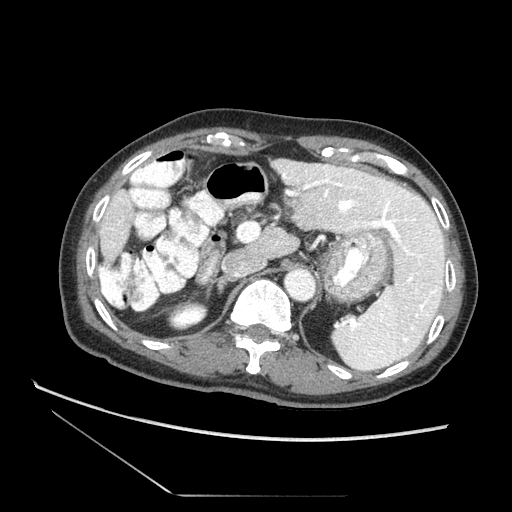
Contrast-enhanced abdominal CT (liver protocol), one axial slice; slice 49 of 73 in the series (ordered by position); soft-tissue window (W 400 / L 40 HU); 2.5 mm slice thickness; 512 × 512 image matrix. Case-level facts recorded for this patient, not image findings: diagnosis: hepatocellular carcinoma (patient treated with transarterial chemoembolisation; whether this scan precedes or follows treatment is not stated here); TNM stage (as recorded): Stage-II.
Annotated regions visible in this slice (semi-automatic segmentation, software-assisted and operator-edited):
- liver parenchyma outside the tumour (the mass and vessels are separate outlines, so this box may not span the whole liver): bounding box <102,161,450,353> (left, top, right, bottom; pixels)
- liver vessels: <294,178,418,253>